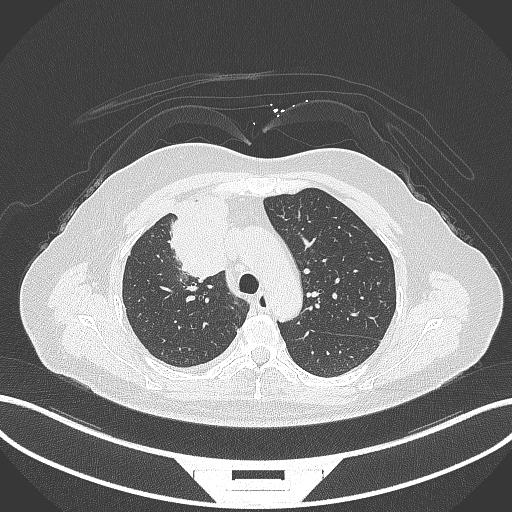
Chest CT, one axial slice; position 211 of 305 along the scan axis; reconstruction kernel B70f; 120 kVp; lung window (W 1500 / L -600 HU); 512 × 512 image matrix, field of view 400 × 400 mm. Female patient, age 52 years. Case-level facts recorded for this patient, not image findings: clinical TNM (as recorded): T3 N1 M1.
Outlined on this slice (bounding box drawn by a radiologist):
- lung tumour (recorded histology: adenocarcinoma): bounding box <166,196,236,284> (left, top, right, bottom; pixels)